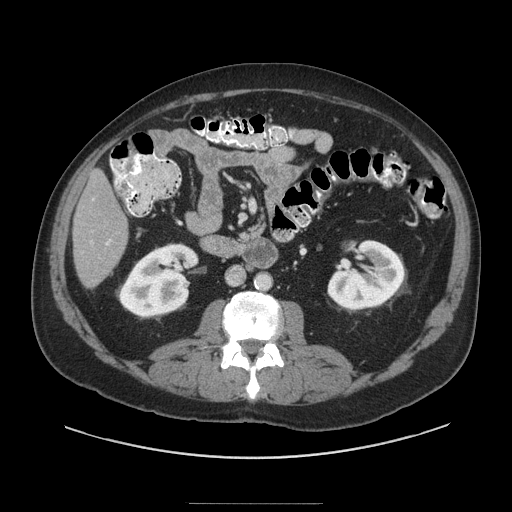
Contrast-enhanced abdominal CT (liver protocol), one axial slice; slice 27 of 91 in the series (ordered by position); soft-tissue window (W 400 / L 40 HU); 2.5 mm slice thickness; 512 × 512 image matrix. Case-level facts recorded for this patient, not image findings: diagnosis: hepatocellular carcinoma (patient treated with transarterial chemoembolisation; whether this scan precedes or follows treatment is not stated here); TNM stage (as recorded): Stage-I; Child-Pugh class: A; tumour differentiation: well differentiated; tumour size: 4 cm.
Structures marked on this image (semi-automatic segmentation, software-assisted and operator-edited):
- liver parenchyma outside the tumour (the mass and vessels are separate outlines, so this box may not span the whole liver): bounding box (x1, y1, x2, y2) in pixels: (72, 170, 128, 286)
- liver vessels: (106, 240, 112, 245)